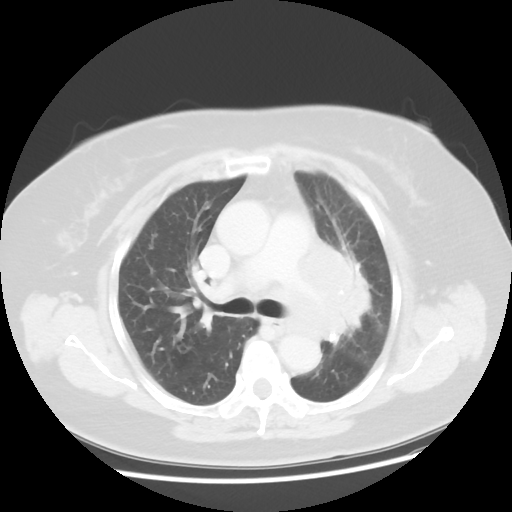
Chest CT, one axial slice; position 29 of 49 along the scan axis; reconstruction kernel STANDARD; 120 kVp; lung window (W 1500 / L -600 HU); 5 mm slice thickness; 512 × 512 image matrix, field of view 374 × 374 mm. Female patient, age 58 years. From the clinical record (not read from this slice): clinical TNM (as recorded): T4 N3 M0; histopathological grade: G3.
Outlined on this slice (bounding box drawn by a radiologist):
- lung tumour (recorded histology: small cell carcinoma): bounding box [x1, y1, x2, y2] px = [277, 240, 372, 369]